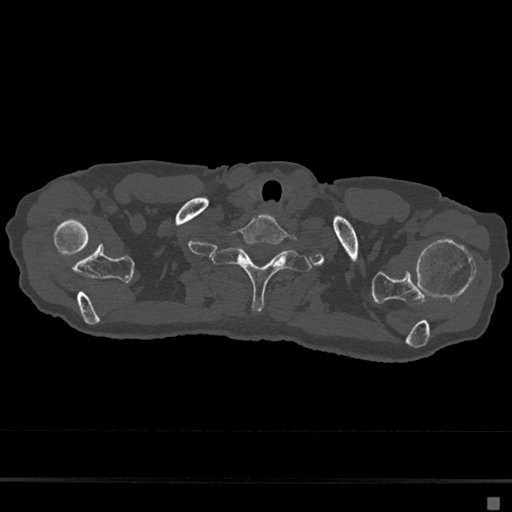
CT including the spine, one axial slice. Position 618 of 797 along the scan axis. Bone window (W 1800 / L 400 HU). 0.5 mm slice thickness. 512 × 512 image matrix, field of view 360 × 360 mm. Patient: female, 68 years. Case-level facts recorded for this patient, not image findings: primary cancer: renal.
Annotated regions visible in this slice (semi-automatic segmentation, software-assisted and operator-edited):
- T1 vertebra: bounding box (x1, y1, x2, y2) in pixels: (212, 241, 312, 311)